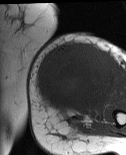
MRI of an extremity soft-tissue mass, one axial slice; slice 26 of 86 in the series (ordered by position); MR volume resampled by the dataset authors to the PET/CT grid (not the native acquisition matrix); 126 × 155 image matrix, field of view 123 × 151 mm. Female patient. Case-level facts recorded for this patient, not image findings: histological type: pleiomorphic leiomyosarcoma; grade: high; site of the primary tumour: left biceps.
Annotated regions visible in this slice (expert contour drawn on MRI and transferred to this co-registered scan by the dataset authors):
- gross tumour volume including surrounding oedema: box from (x=36, y=42) to (x=115, y=116) px
- gross tumour volume (mass): (x=36, y=42)–(x=115, y=114)